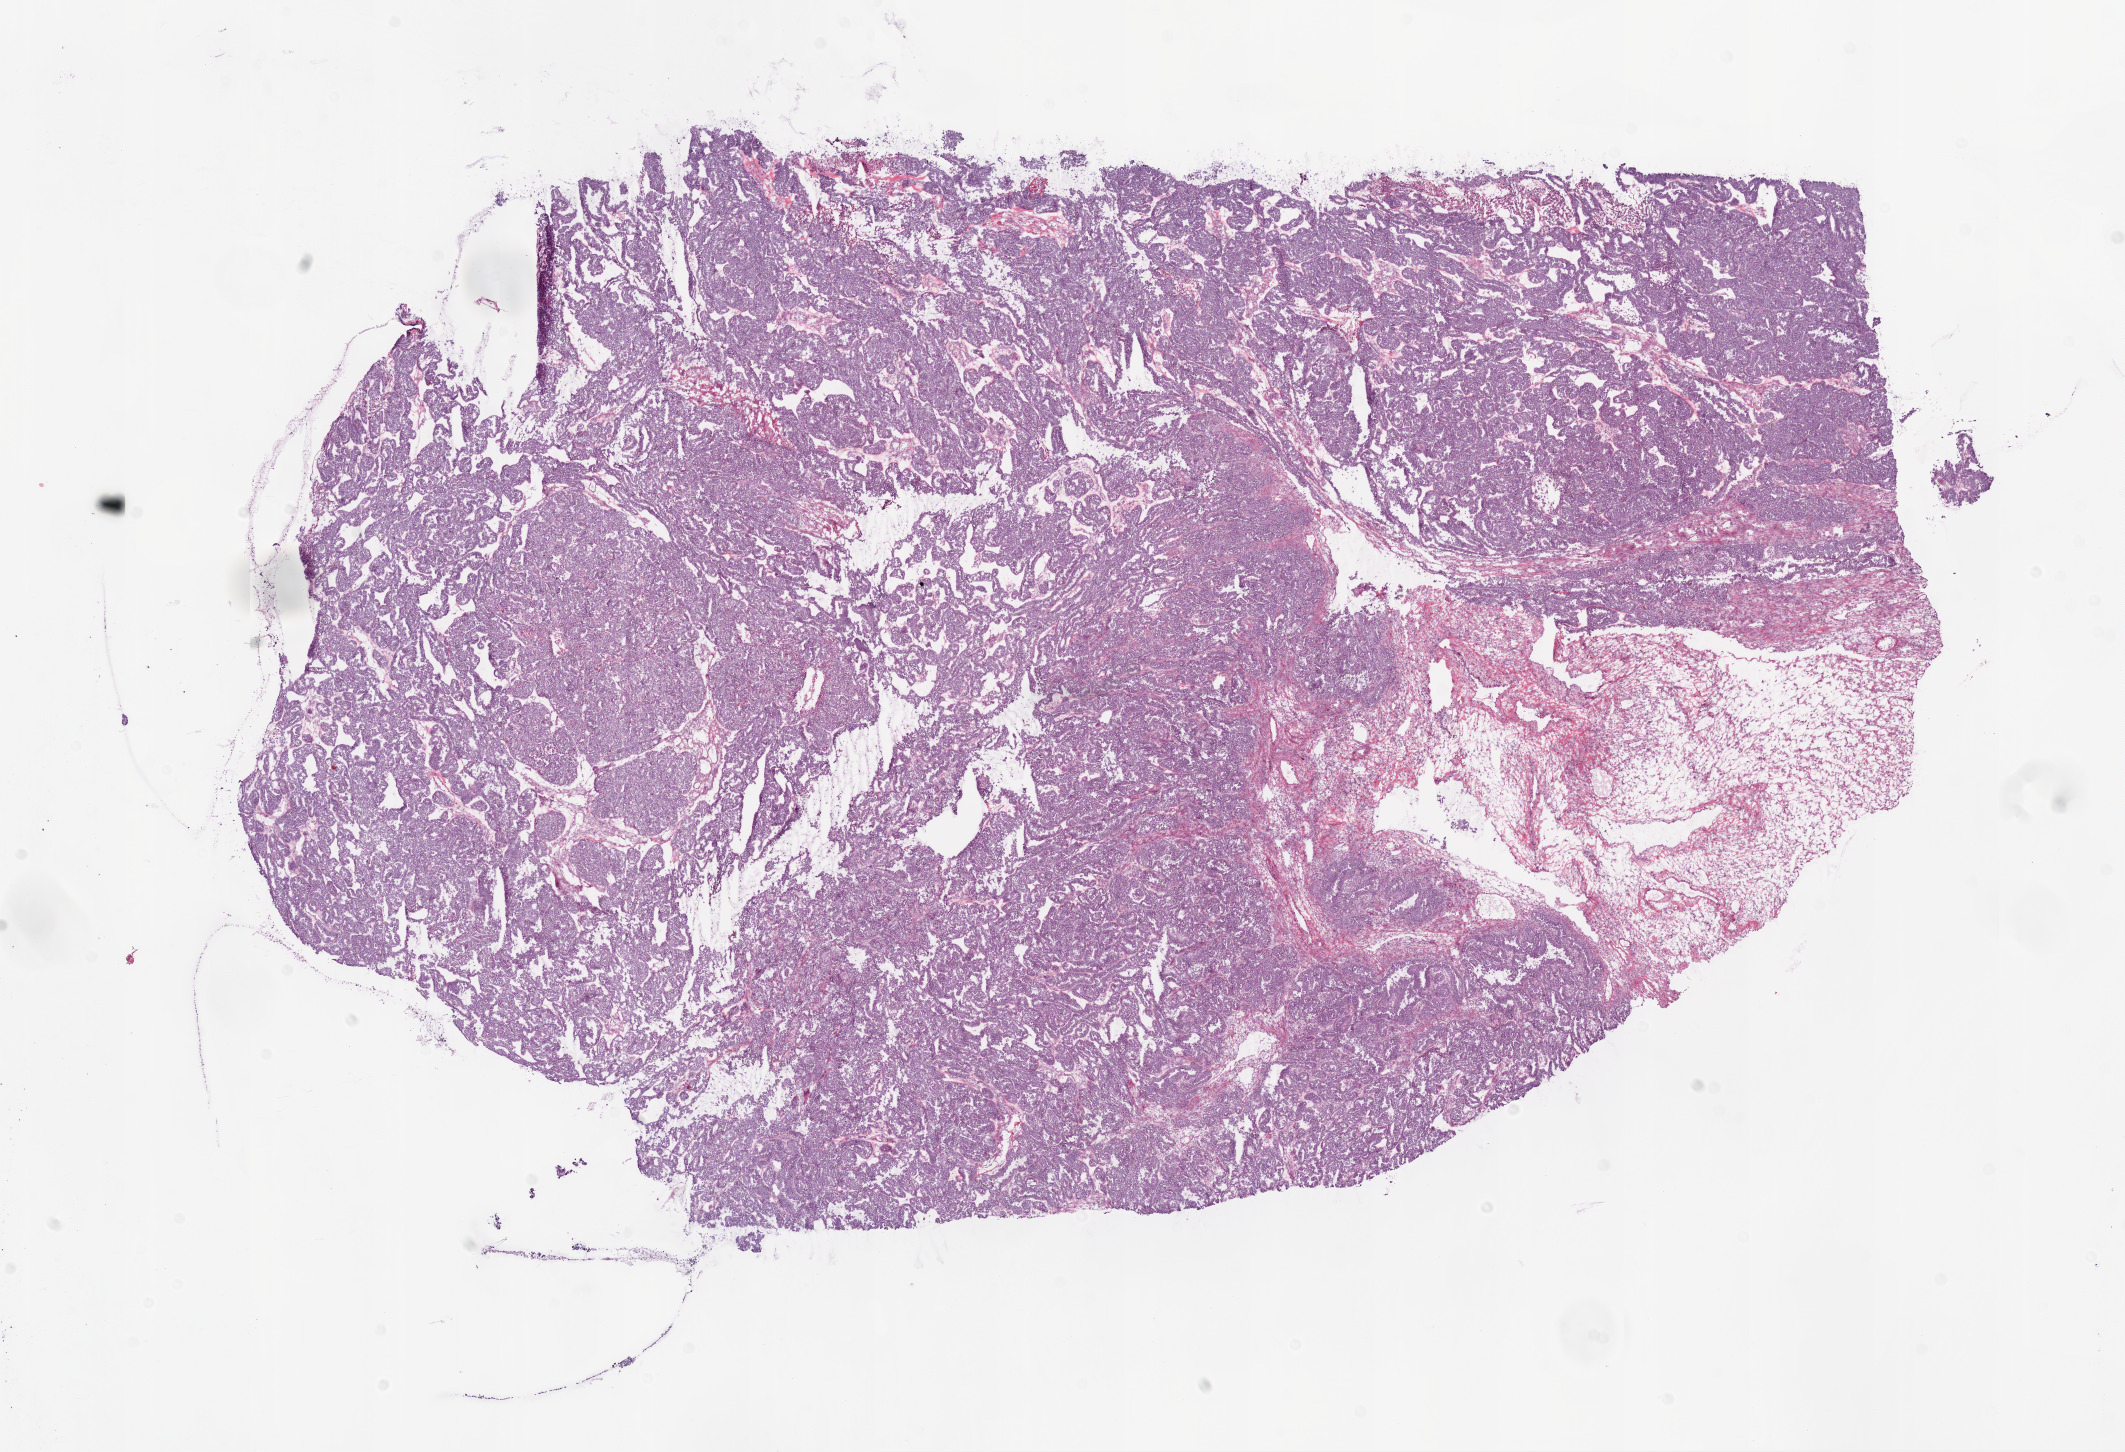
Digitized Hematoxylin and eosin (H&E) stained tissue section (whole slide) — a low-resolution overview of the entire scanned area, about 17.1 x 11.7 mm (acquisition: 20x scan). Frozen section from the top of the tissue portion. Sample: primary tumour, ovary. Female patient; age at initial diagnosis 51 years. Histologic grade: G3 (poorly differentiated). Composition of this section per pathologist review: tumour cells 95%, tumour nuclei 95%, normal cells 0%, stromal cells 5%, necrosis 0%.
Laterality: bilateral. Diagnosis: Serous cystadenocarcinoma, NOS. FIGO stage: IIIB.